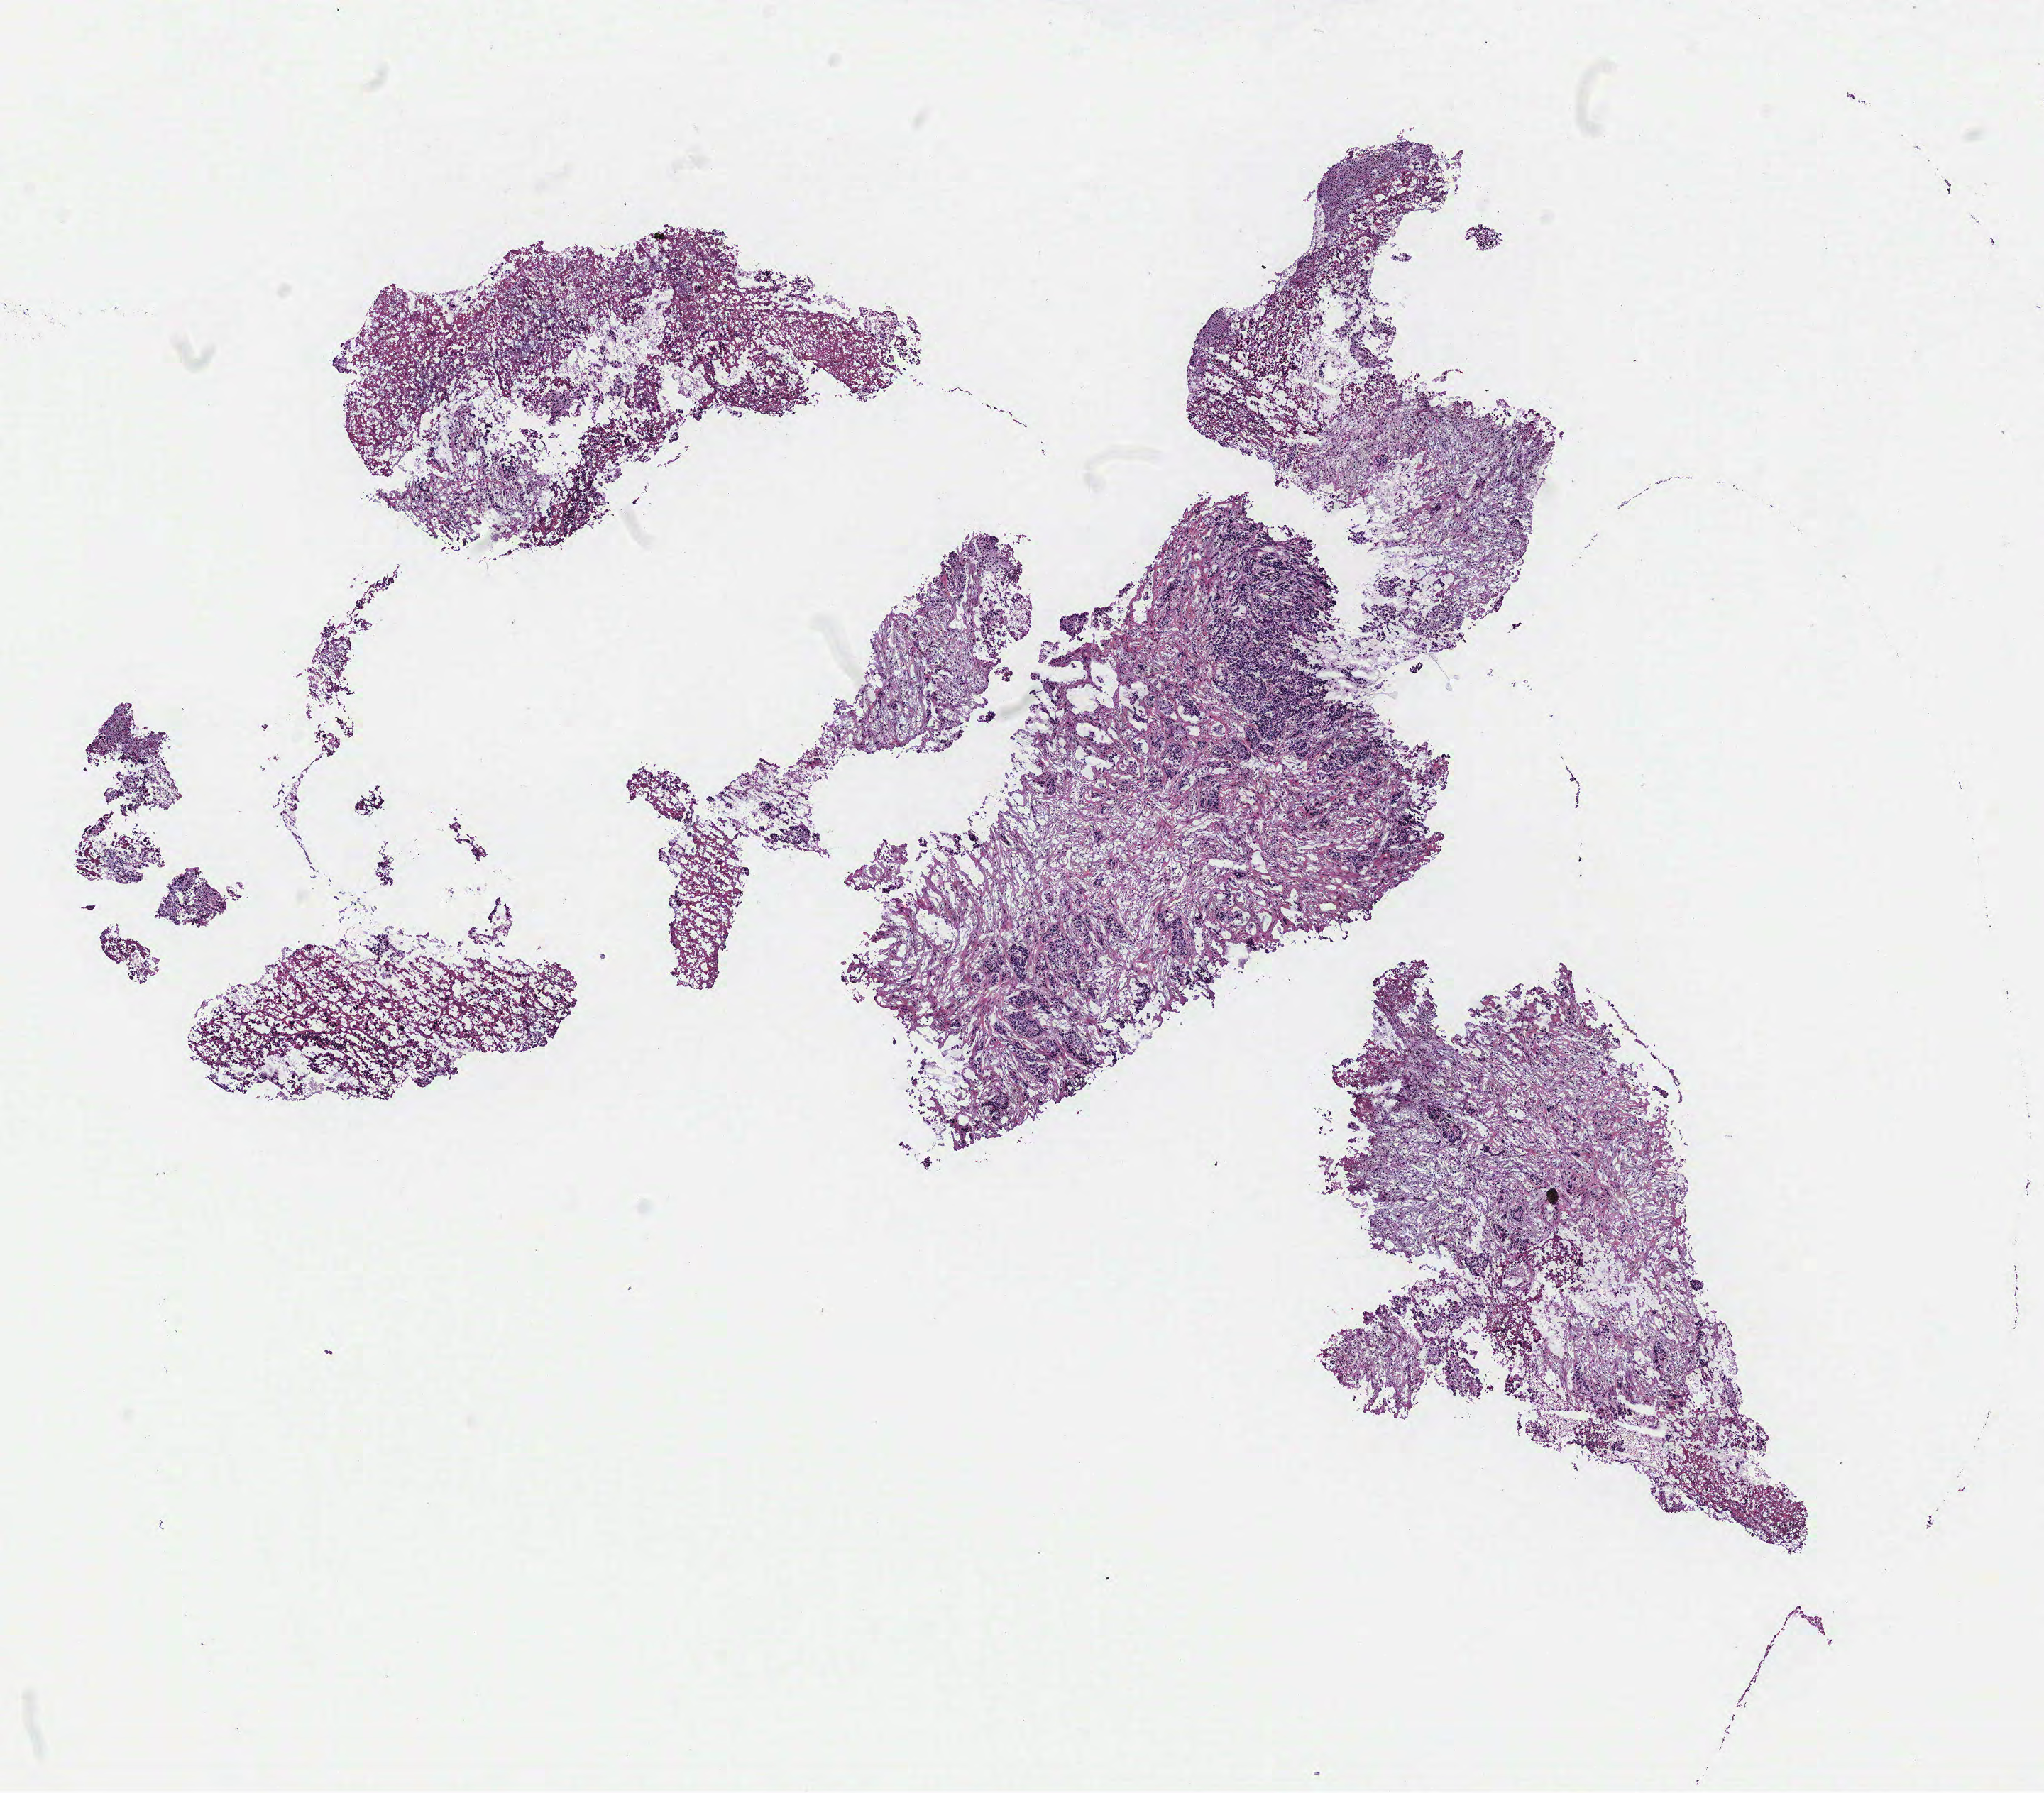
Hematoxylin and eosin (H&E) stained whole-slide image, a low-resolution overview of the entire scanned area, about 11.5 x 10.1 mm (slide scanned at 40x); tumour tissue sample, ovary. 55-year-old female patient.
• patient diagnosis (cohort enrolment): ovarian cancer (ovary)